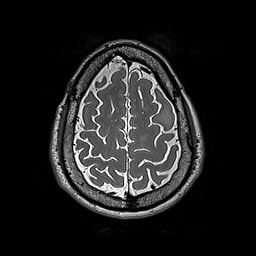
Brain MRI from a brain-tumour surgery series, one axial slice; slice 57 of 192 in the series (ordered by position); 256 × 256 image matrix, field of view 250 × 250 mm. From the clinical record (not read from this slice): histopathology: Astrocytoma; WHO grade: 2; IDH mutation: yes; tumour location: Left Frontal.
Structures marked on this image (outlined manually by an expert reader):
- tumour: bounding box <158,107,171,127> (left, top, right, bottom; pixels)